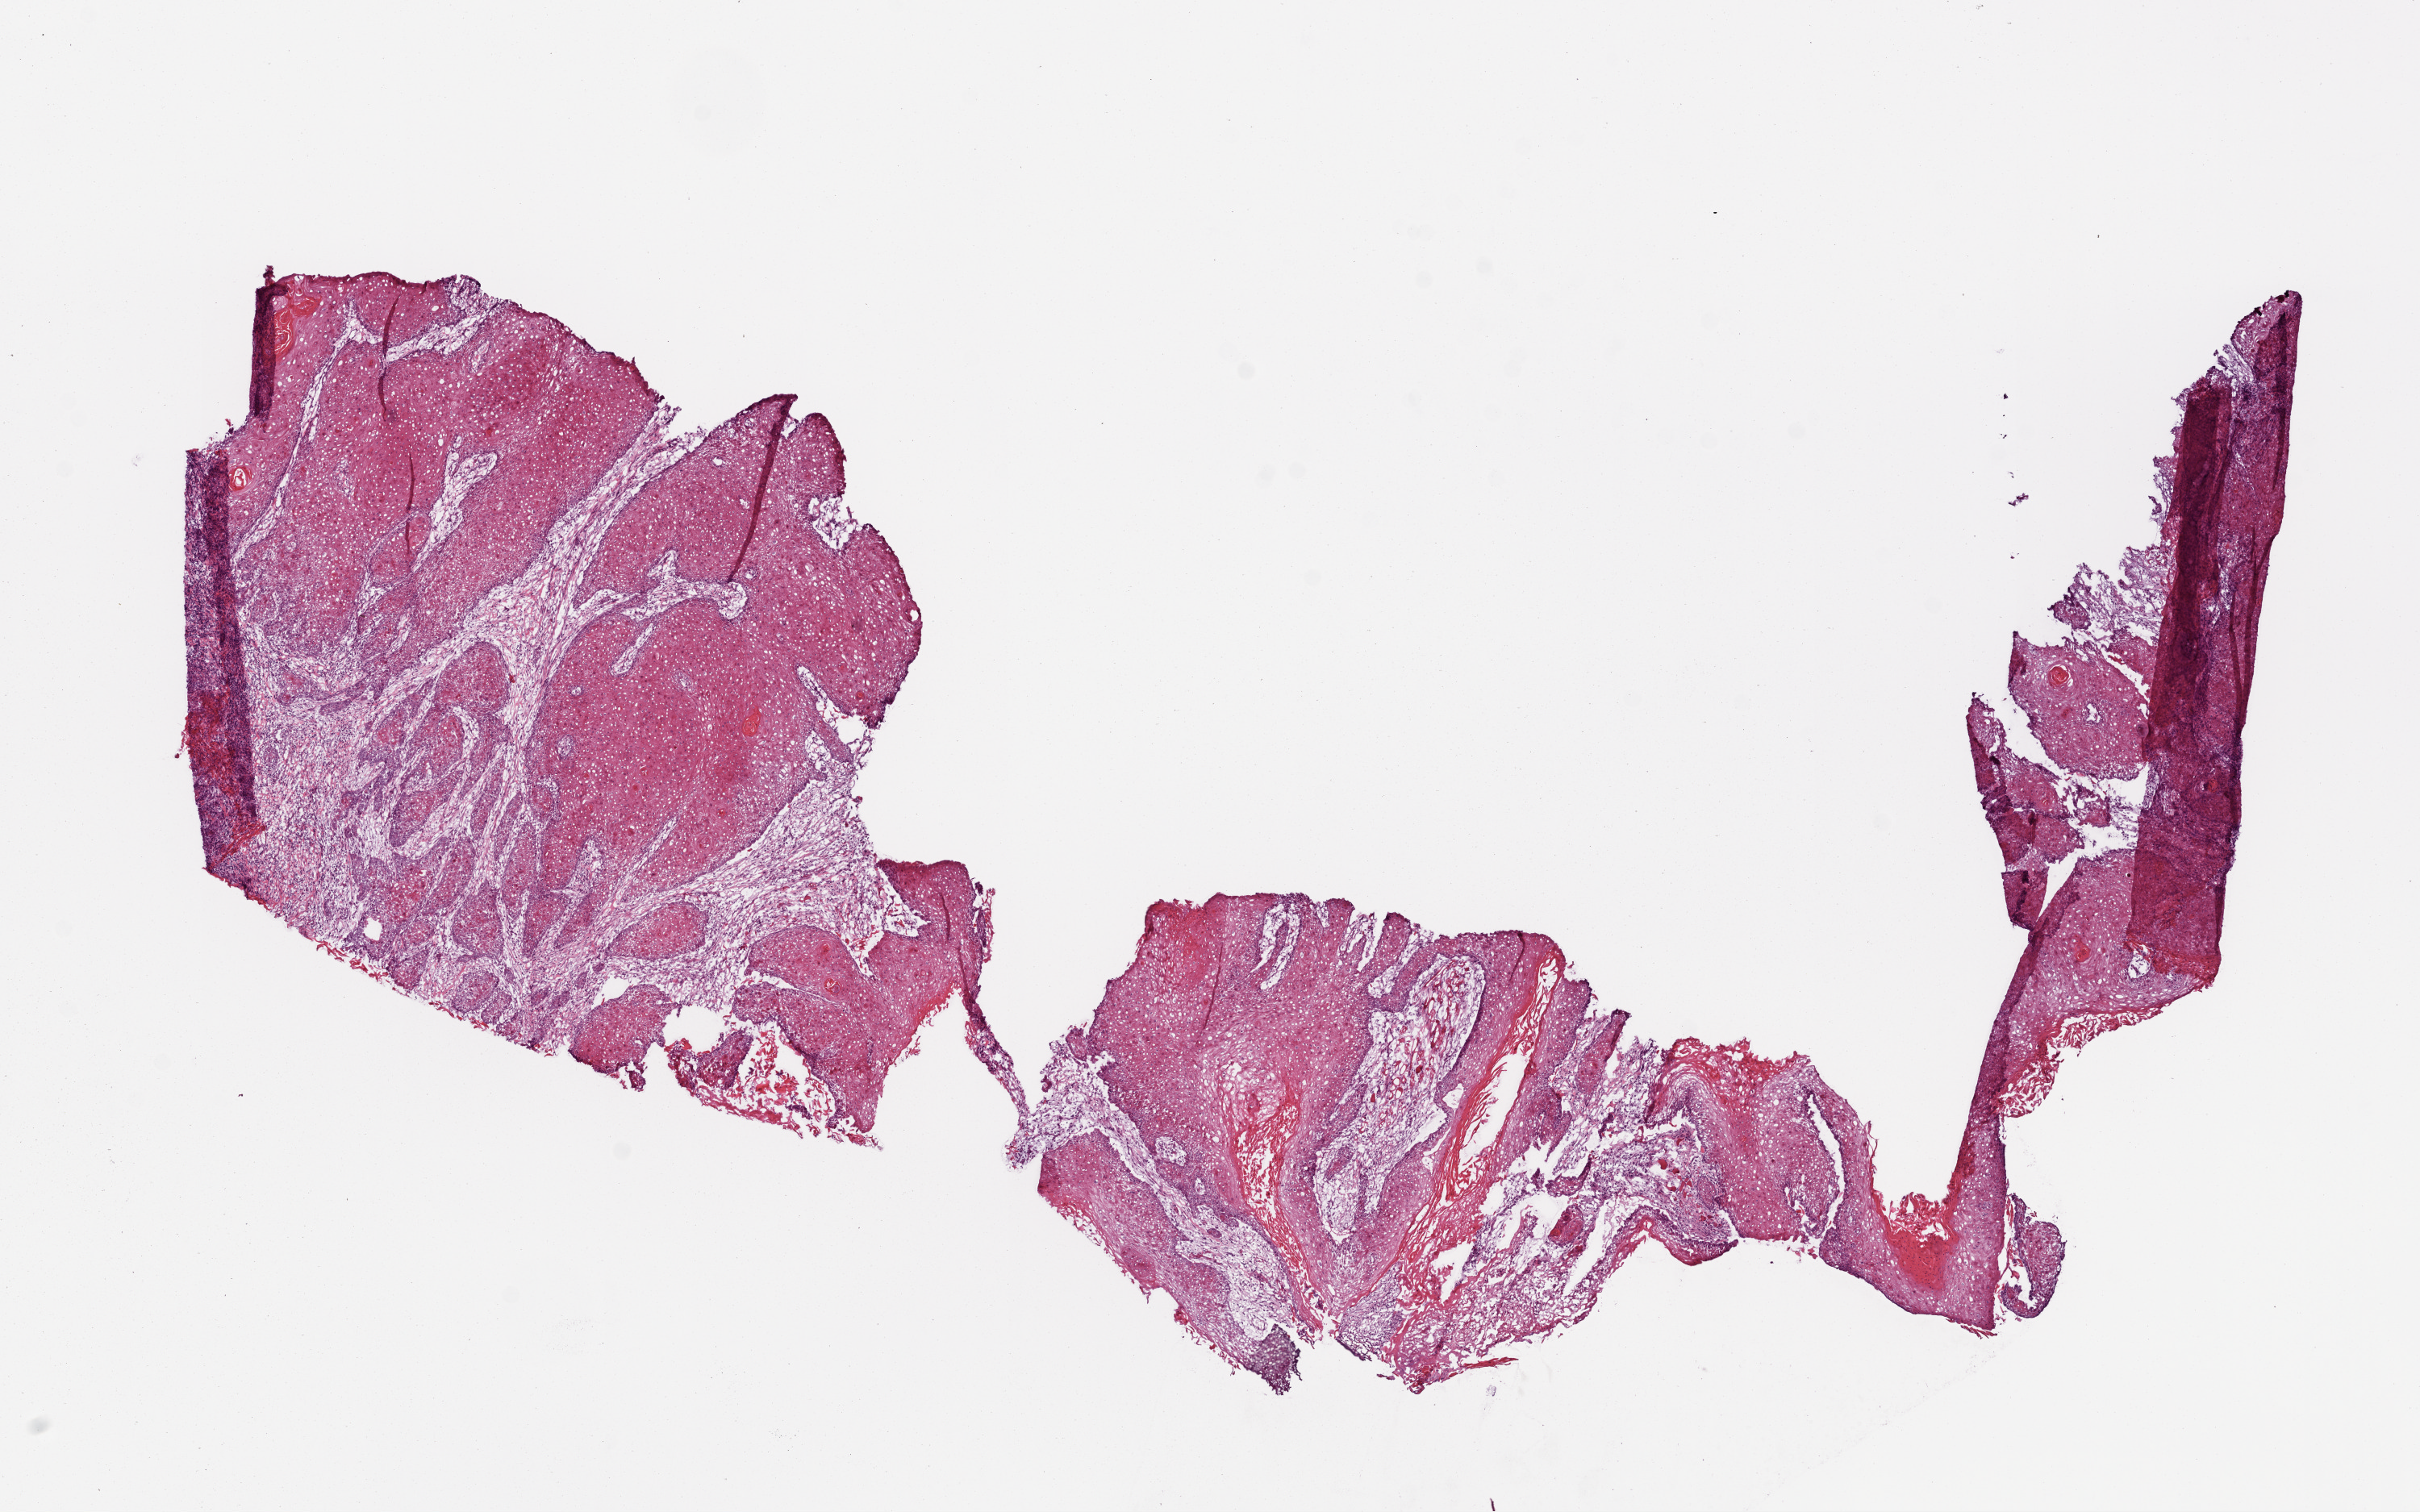
H&E whole-slide image, whole scanned area (about 12.0 x 7.5 mm) shown as a low-resolution overview; frozen section; primary tumour sample from the head and neck. Patient: female, age at initial diagnosis 55 years. Histologic grade: G1 (well differentiated). Pathologist review of this section (percent, as recorded): tumour cells 75%, tumour nuclei 75%, normal cells 10%, stromal cells 15%, necrosis 0%.
TNM: T1 N0. AJCC pathologic stage: I (7th edition). Pathologic diagnosis: Squamous cell carcinoma, NOS (floor of mouth, NOS).